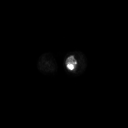
FDG PET of an extremity soft-tissue mass (from a PET/CT study), one axial slice; slice 144 of 223 in the series (ordered by position); 3.27 mm slice thickness; 128 × 128 image matrix. Patient: female, 70 years. From the clinical record (not read from this slice): histological type: extraskeletal high grade osteogenic sarcoma; grade: high; site of the primary tumour: left calf.
Structures marked on this image (expert contour drawn on MRI and transferred to this co-registered scan by the dataset authors):
- gross tumour volume (mass): bounding box [x1, y1, x2, y2] px = [66, 57, 77, 70]